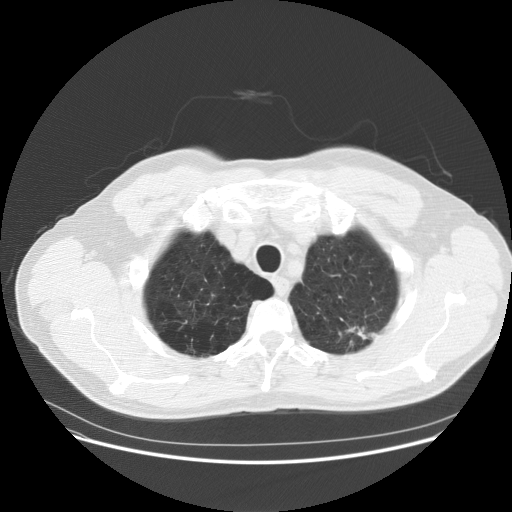
Low-dose screening chest CT, one axial slice; slice 143 of 158 in the series (ordered by position); reconstruction kernel STANDARD; 120 kVp; lung window (W 1500 / L -600 HU); 2.5 mm slice thickness; 512 × 512 image matrix, field of view 400 × 400 mm.
Annotated regions visible in this slice (expert manual segmentation):
- lesion 1 (tumor, upper lobe of left lung): bounding box [x1, y1, x2, y2] px = [347, 326, 377, 340]